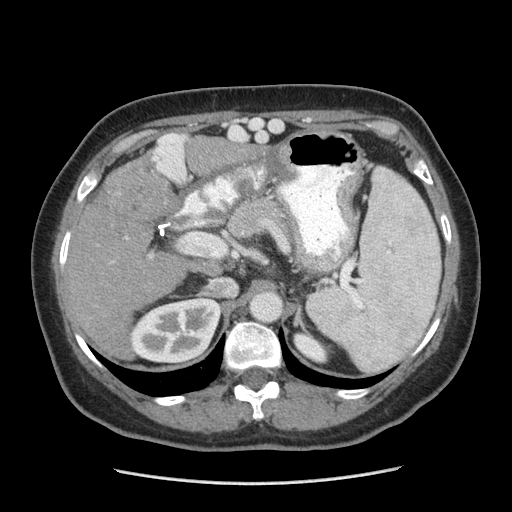
Contrast-enhanced abdominal CT (liver protocol), one axial slice. Slice 151 of 185 in the series (ordered by position). Reconstruction kernel STANDARD. Soft-tissue window (W 400 / L 40 HU). 2.5 mm slice thickness. 512 × 512 image matrix. From the clinical record (not read from this slice): diagnosis: hepatocellular carcinoma (patient treated with transarterial chemoembolisation; whether this scan precedes or follows treatment is not stated here); TNM stage (as recorded): Stage-I; Child-Pugh class: A; tumour differentiation: poorly differentiated; tumour nodularity: uninodular.
Annotated regions visible in this slice (semi-automatic segmentation, software-assisted and operator-edited):
- liver parenchyma outside the tumour (the mass and vessels are separate outlines, so this box may not span the whole liver): bounding box (x1, y1, x2, y2) in pixels: (62, 132, 241, 354)
- mass: (103, 160, 172, 222)
- liver vessels: (68, 133, 186, 258)